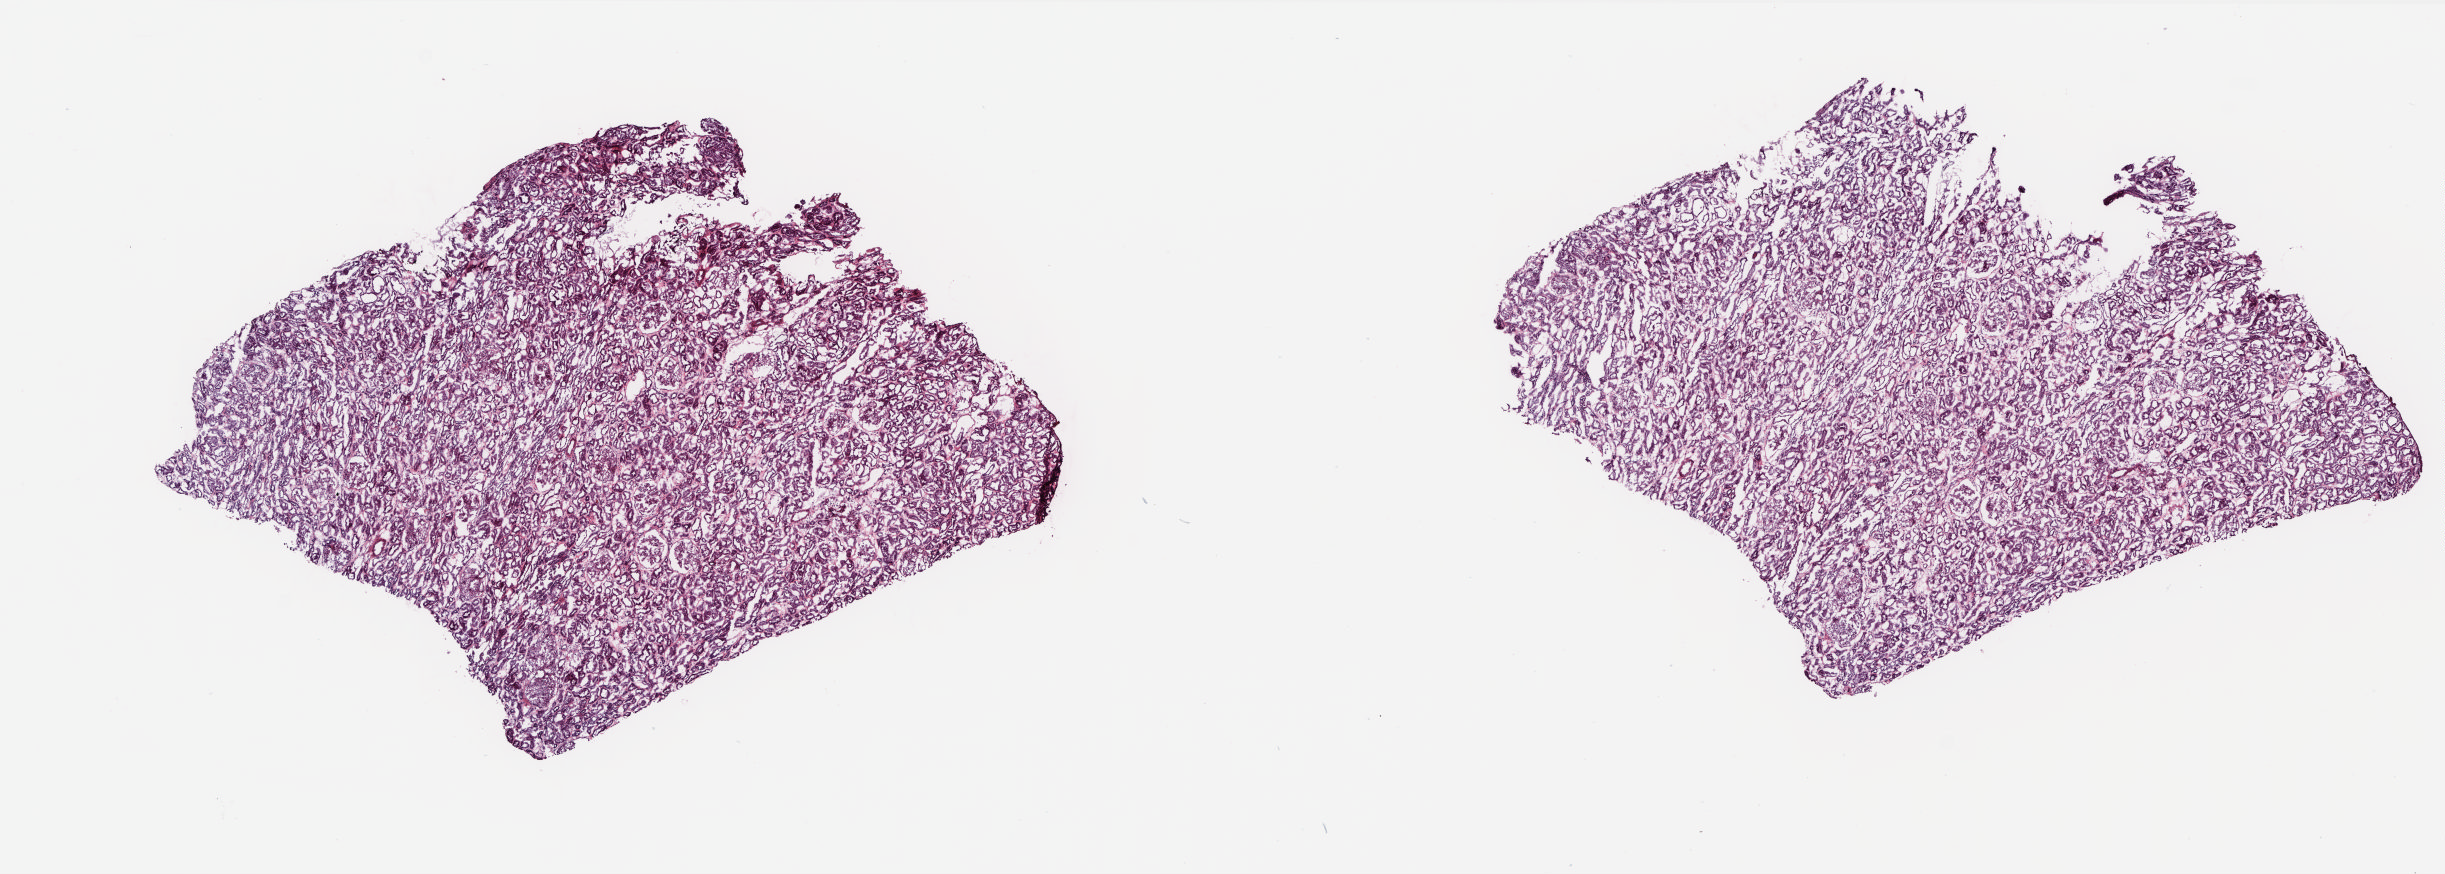
Whole-slide histology image, H&E — shown as a low-resolution overview of the whole scanned area (about 19.7 x 7.0 mm, acquisition: 20x scan). Frozen section from the top of the tissue portion. Sample: solid tissue normal (non-tumour tissue), kidney. Female patient; age at initial diagnosis 49 years.
This section: solid tissue normal (non-tumour) sample from the same patient. Patient diagnosis: Renal cell carcinoma, NOS.